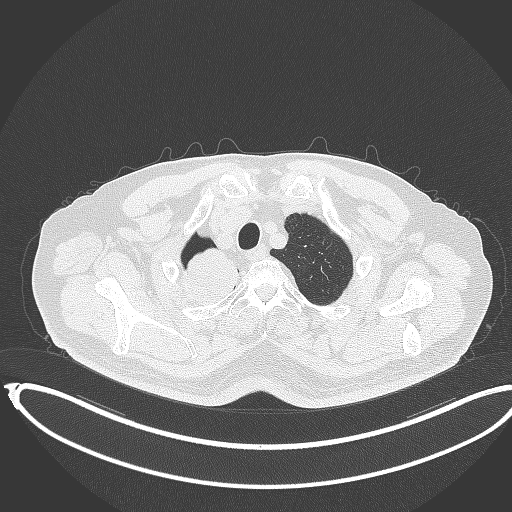
Chest CT, one axial slice. Lung window (W 1500 / L -600 HU). 512 × 512 image matrix. Male patient, age 68 years. Case-level facts recorded for this patient, not image findings: clinical TNM (as recorded): T2a N0 M0.
Outlined on this slice (bounding box drawn by a radiologist):
- lung tumour (recorded histology: adenocarcinoma): bounding box [x1, y1, x2, y2] px = [172, 243, 239, 307]